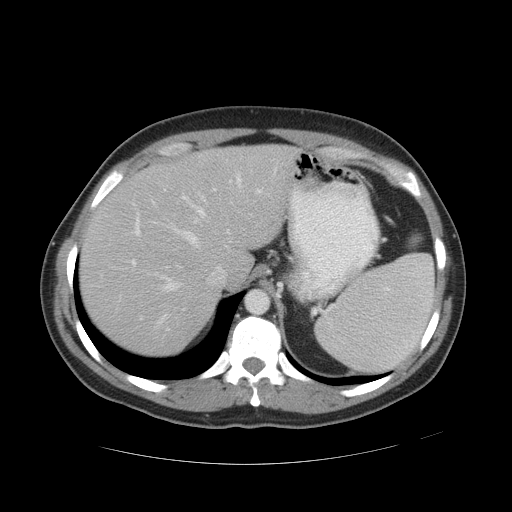
Contrast-enhanced abdominal CT, one axial slice. Slice 38 of 49 in the series (ordered by position). Reconstruction kernel STANDARD. 120 kVp. Intravenous contrast given. Soft-tissue window (W 400 / L 40 HU). 512 × 512 image matrix, field of view 422 × 422 mm. Male patient, age 42 years. From the clinical record (not read from this slice): diagnosis: colorectal cancer liver metastases, imaged before liver resection; multiple liver metastases: yes; largest metastasis: 2.8 cm; disease in both lobes: yes.
Outlined on this slice (outlined manually by an expert reader):
- hepatic veins: box from (x=128, y=172) to (x=242, y=324) px
- liver: (x=80, y=146)–(x=294, y=356)
- planned liver remnant (the part of the liver to remain after resection): (x=80, y=146)–(x=294, y=356)
- portal vein (with intrahepatic branches): (x=131, y=180)–(x=262, y=320)